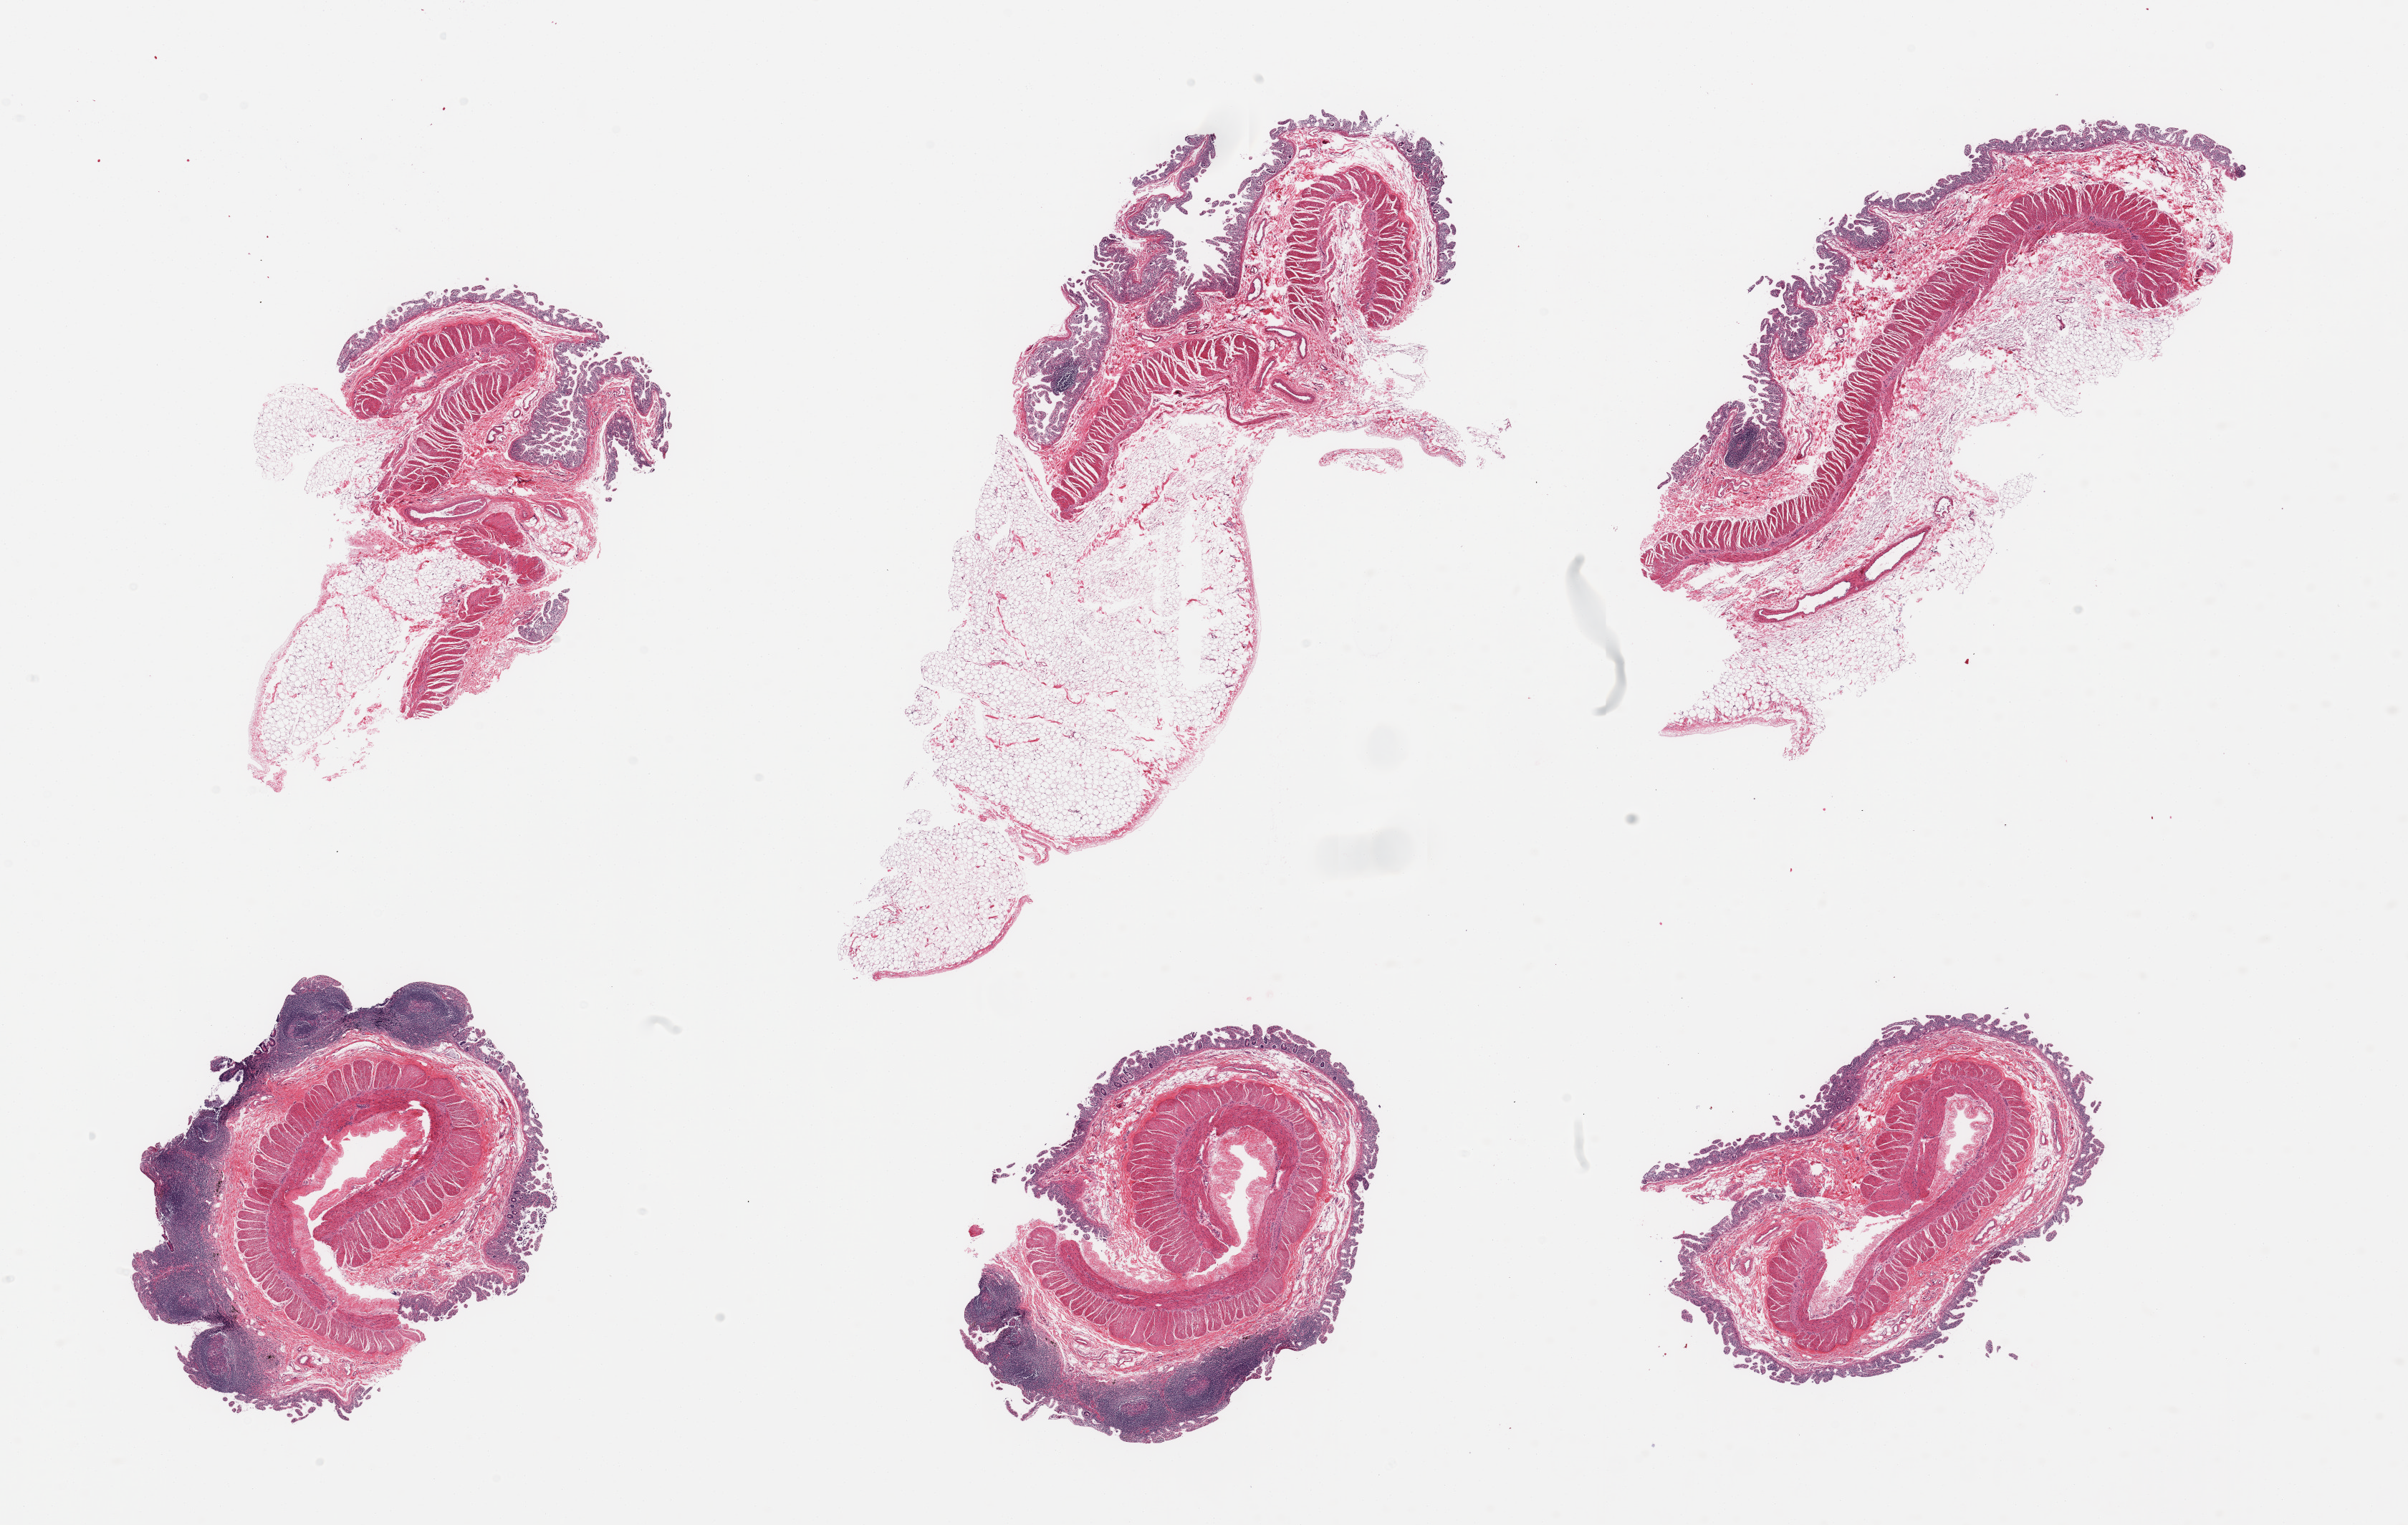
Digitized haematoxylin and eosin-stained section, whole scanned area (about 26.6 x 16.8 mm) shown as a low-resolution overview. PAXgene-fixed paraffin-embedded (PFPE) section. Target tissue: ileum. Tissue donor sample. Donor sex: male.
Pathologist's review note for this sample: 6 pieces; full thickness sections with residual attached fat, several good lymphoid follicles in 2 of 6 pieces.